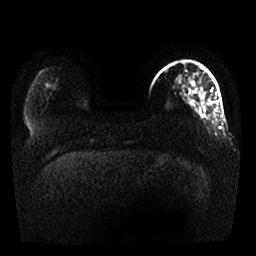
Breast MRI, one axial slice. Position 4 of 25 along the scan axis. Diffusion-weighted series; image 2 of 4 stored at this slice position (different b-values; order by instance number). 1.5 T. 4 mm slice thickness. 256 × 256 image matrix, field of view 330 × 330 mm. Female patient.
Outlined on this slice (expert manual segmentation):
- tumour on diffusion-weighted imaging: bounding box <189,81,193,92> (left, top, right, bottom; pixels)